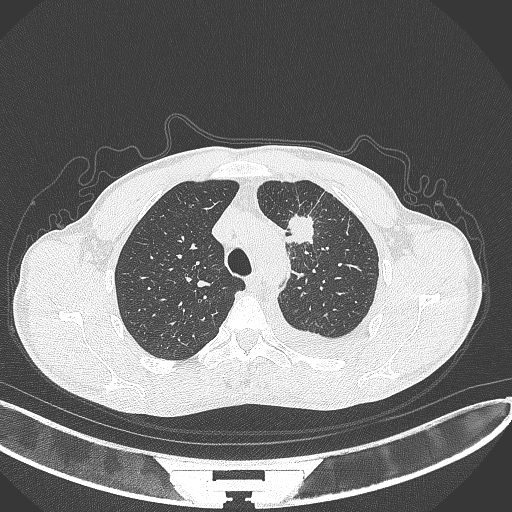
Chest CT, one axial slice; position 263 of 371 along the scan axis; 120 kVp; lung window (W 1500 / L -600 HU); 512 × 512 image matrix. Patient: male, 49 years. From the clinical record (not read from this slice): clinical TNM (as recorded): T1c N1 M1.
Annotated regions visible in this slice (rectangle marked by the reading radiologist):
- lung tumour (recorded histology: adenocarcinoma): bounding box (x1, y1, x2, y2) in pixels: (285, 205, 317, 248)